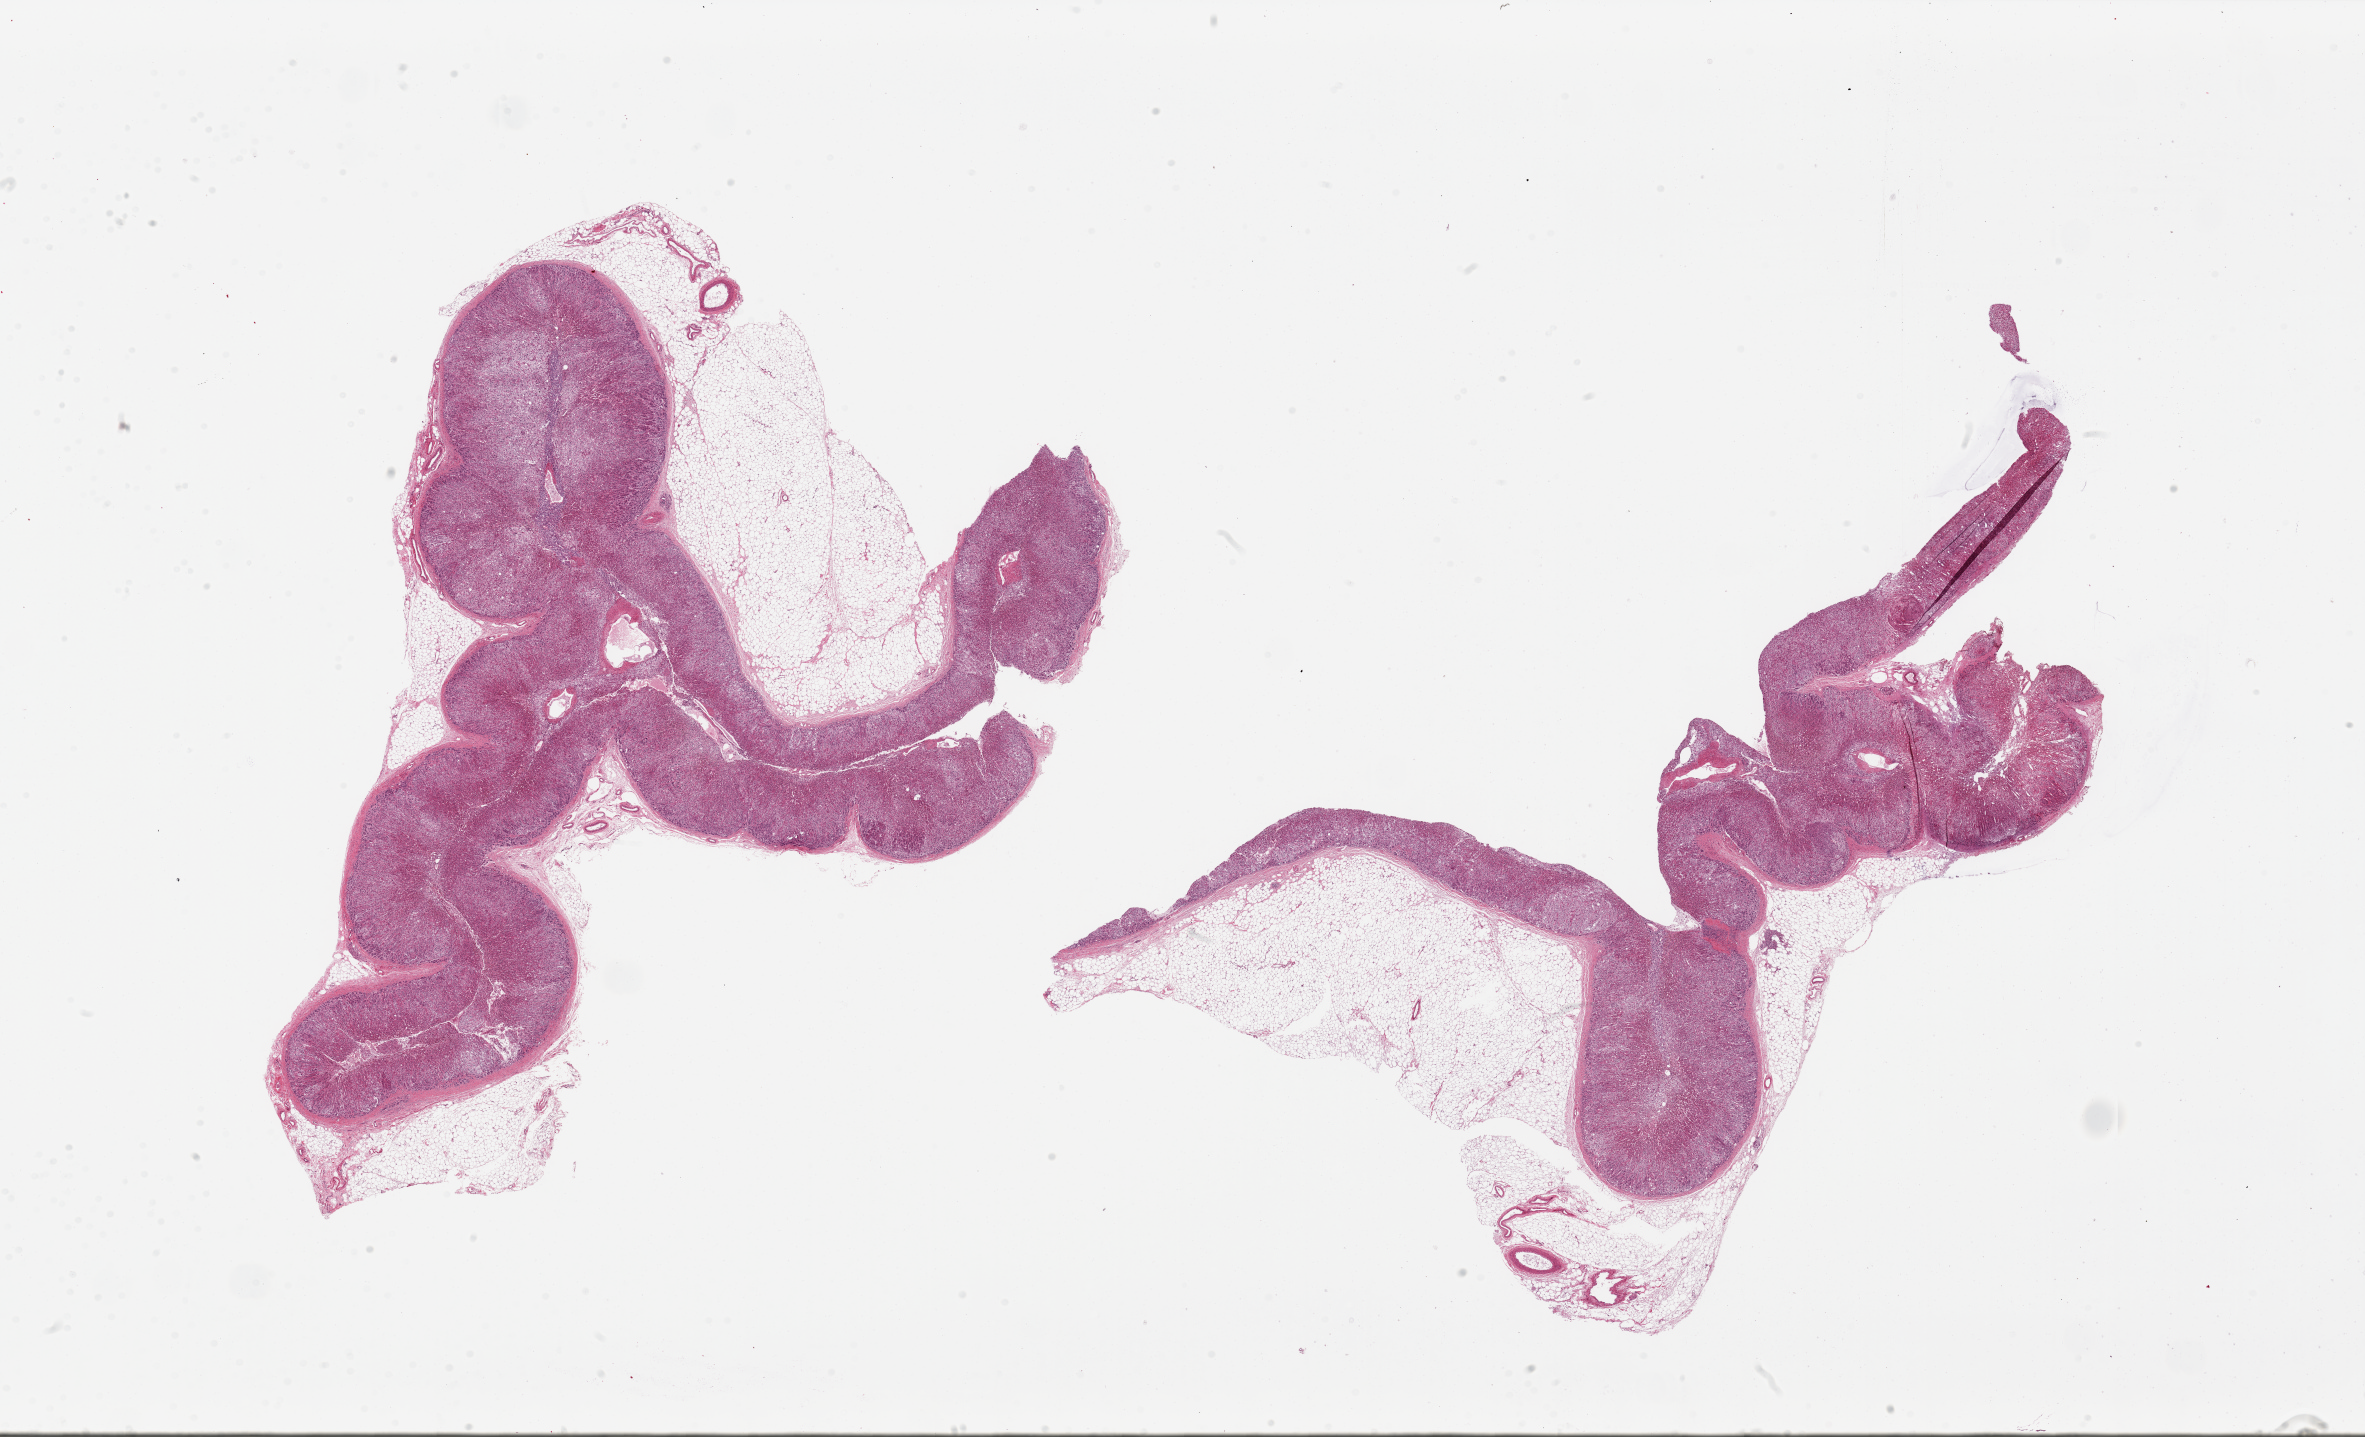
Haematoxylin and eosin whole-slide image, brightfield, shown as a low-resolution overview of the whole scanned area (about 37.4 x 22.7 mm, from a 20x scan); PAXgene-fixed paraffin-embedded (PFPE) section; target tissue: adrenal gland; donor tissue sample. Female donor.
Reviewer comment on this tissue sample: 2 pieces, 17x12 & 18x14mm; 99% cortex, 1% medulla; Remarkably well preserved, adherent fat ~30% of both aliquots up to 3mm thick.